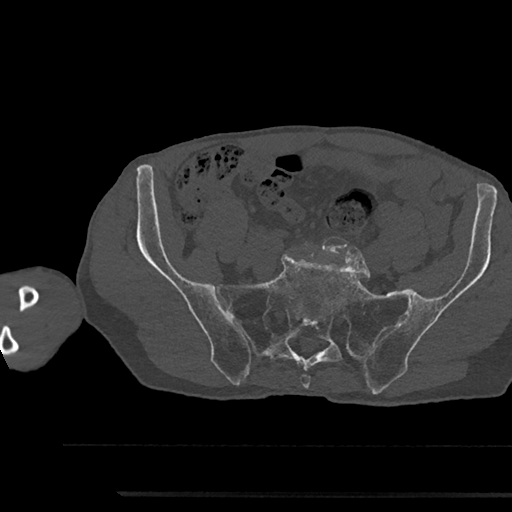
CT including the spine, one axial slice. Position 273 of 797 along the scan axis. Reconstruction kernel Br40s/3. 120 kVp. Bone window (W 1800 / L 400 HU). 0.5 mm slice thickness. 512 × 512 image matrix. Patient: male, 79 years. Case-level facts recorded for this patient, not image findings: primary cancer: prostate.
Annotated regions visible in this slice (semi-automatically segmented with operator editing):
- L5 vertebra: bounding box <303,240,314,248> (left, top, right, bottom; pixels)